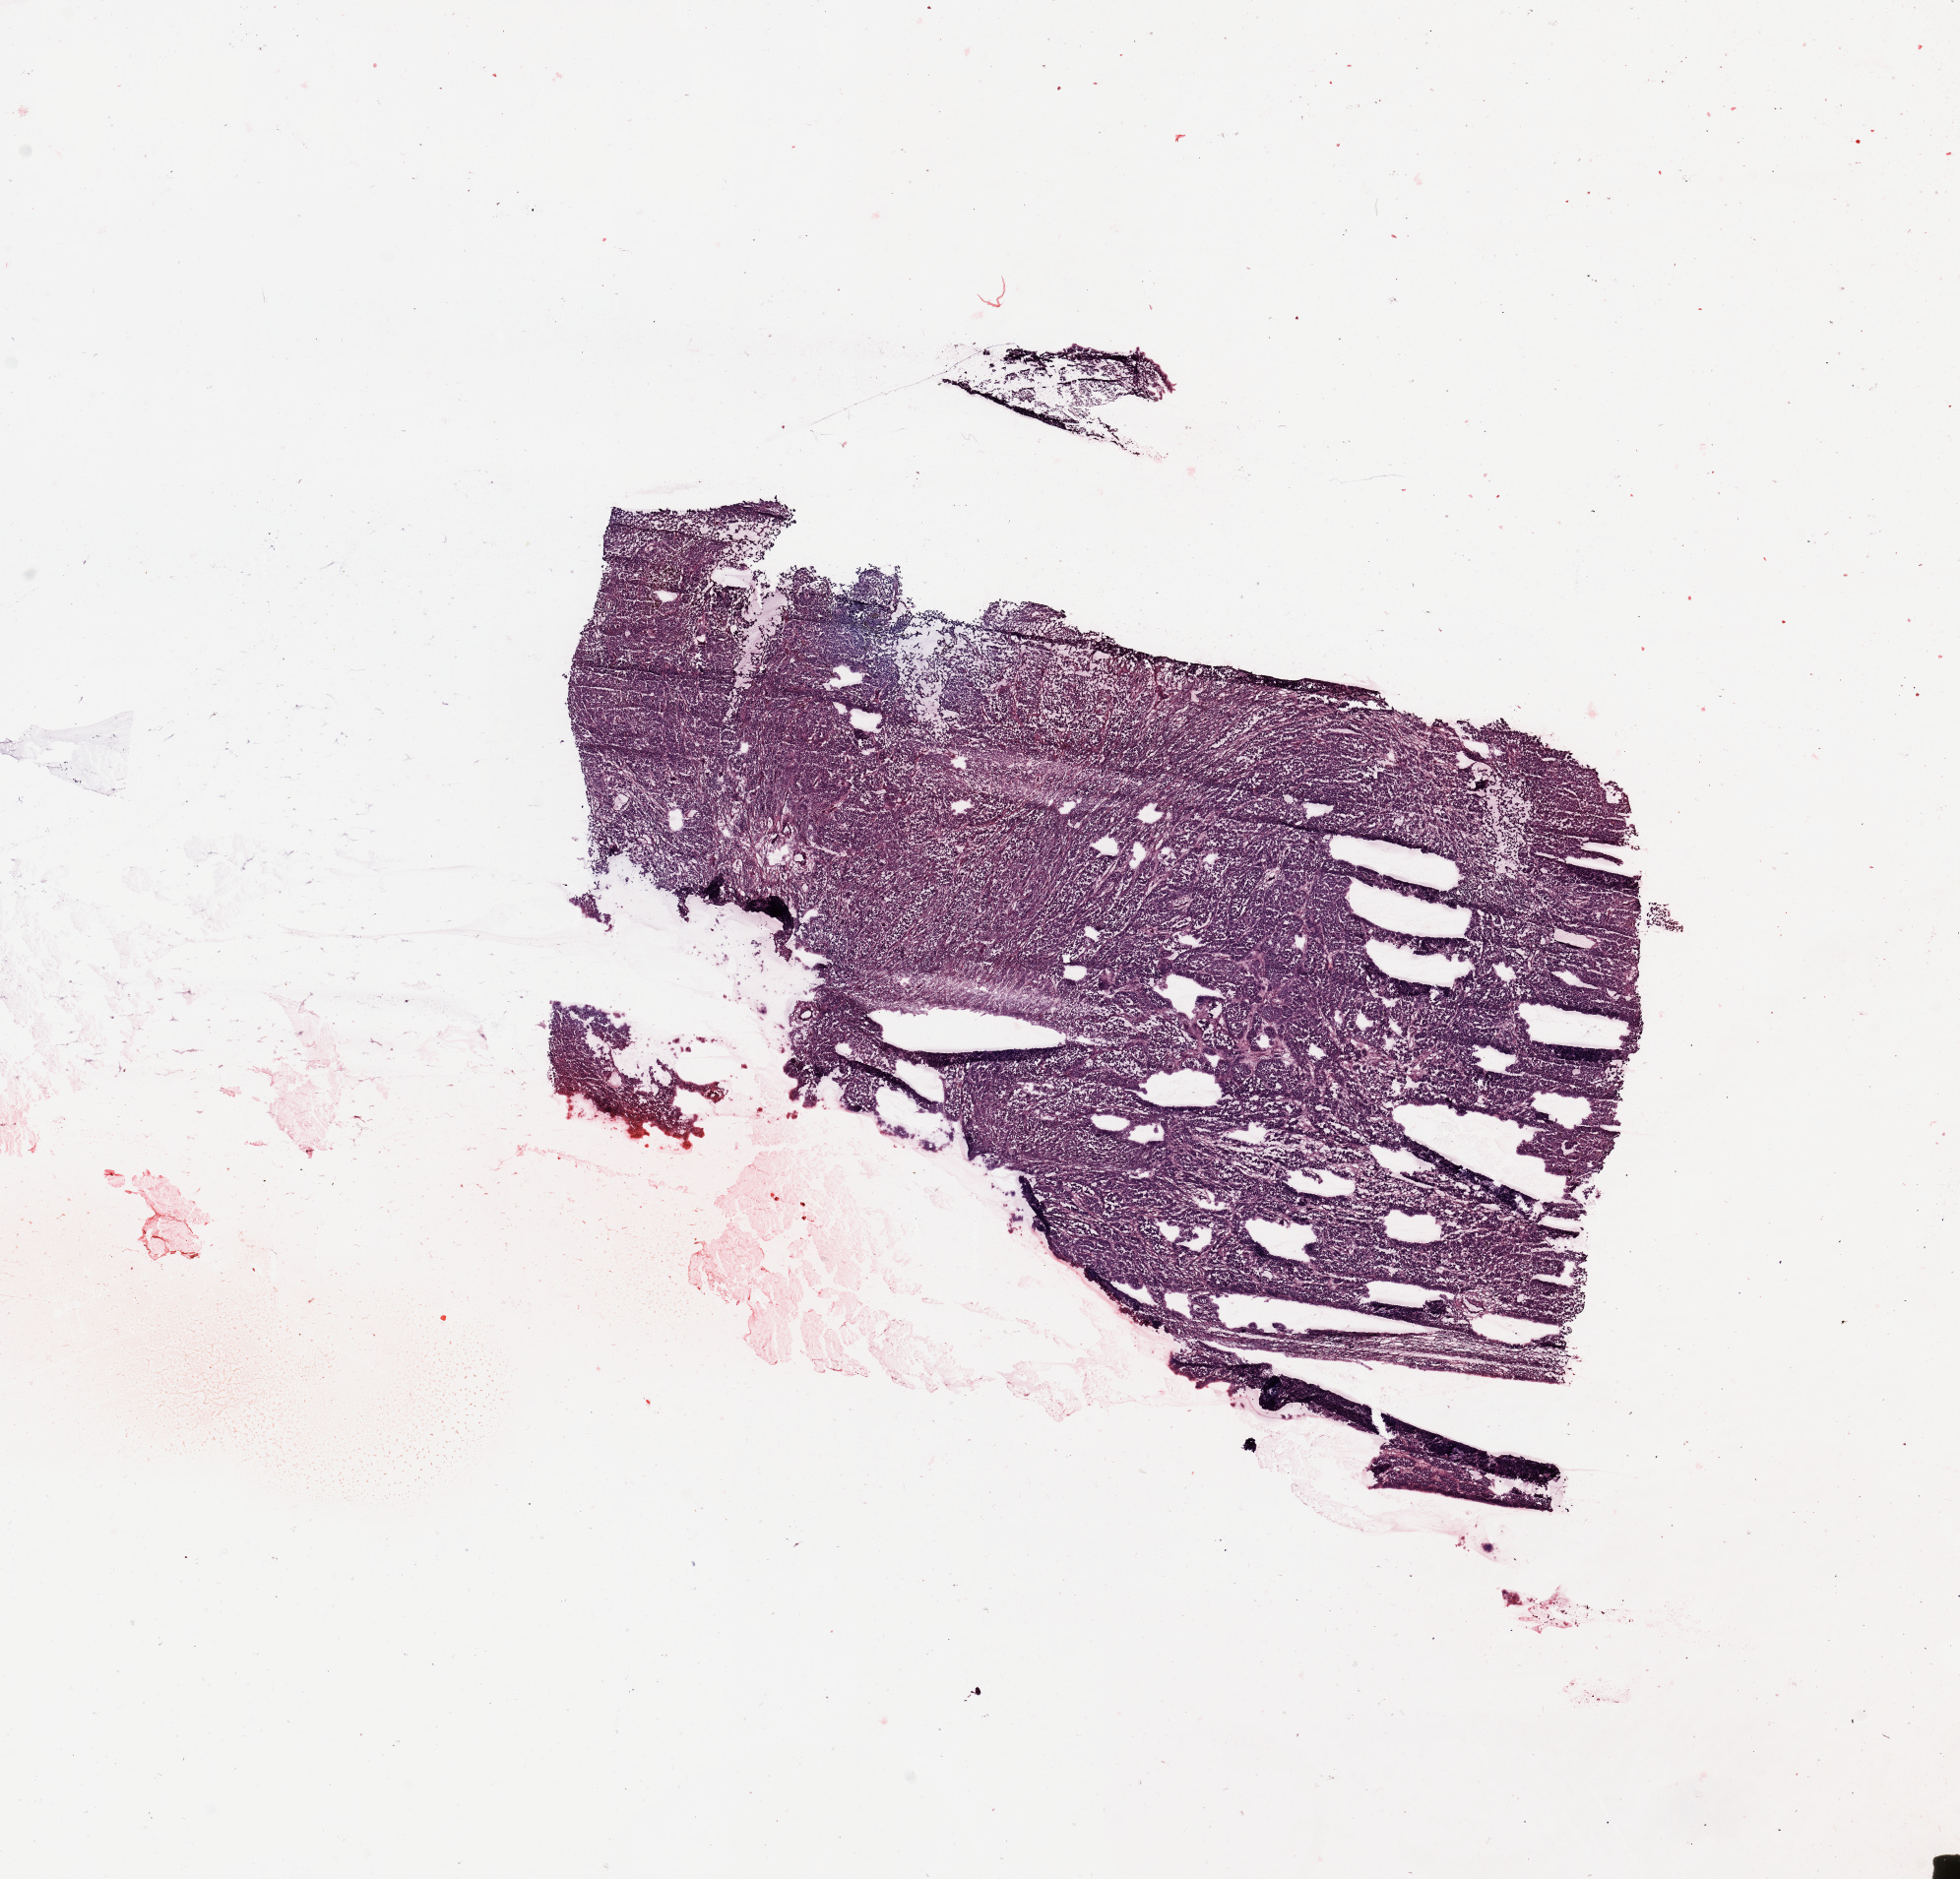
H&E-stained whole-slide image — whole scanned area (about 15.8 x 15.1 mm, acquisition: 20x scan) shown as a low-resolution overview. Melanoma tumour tissue; sampled site not recorded. Female, 51 y/o.
Primary tumour site (as recorded): extremities. Patient diagnosis (cohort enrolment): cutaneous melanoma (skin).